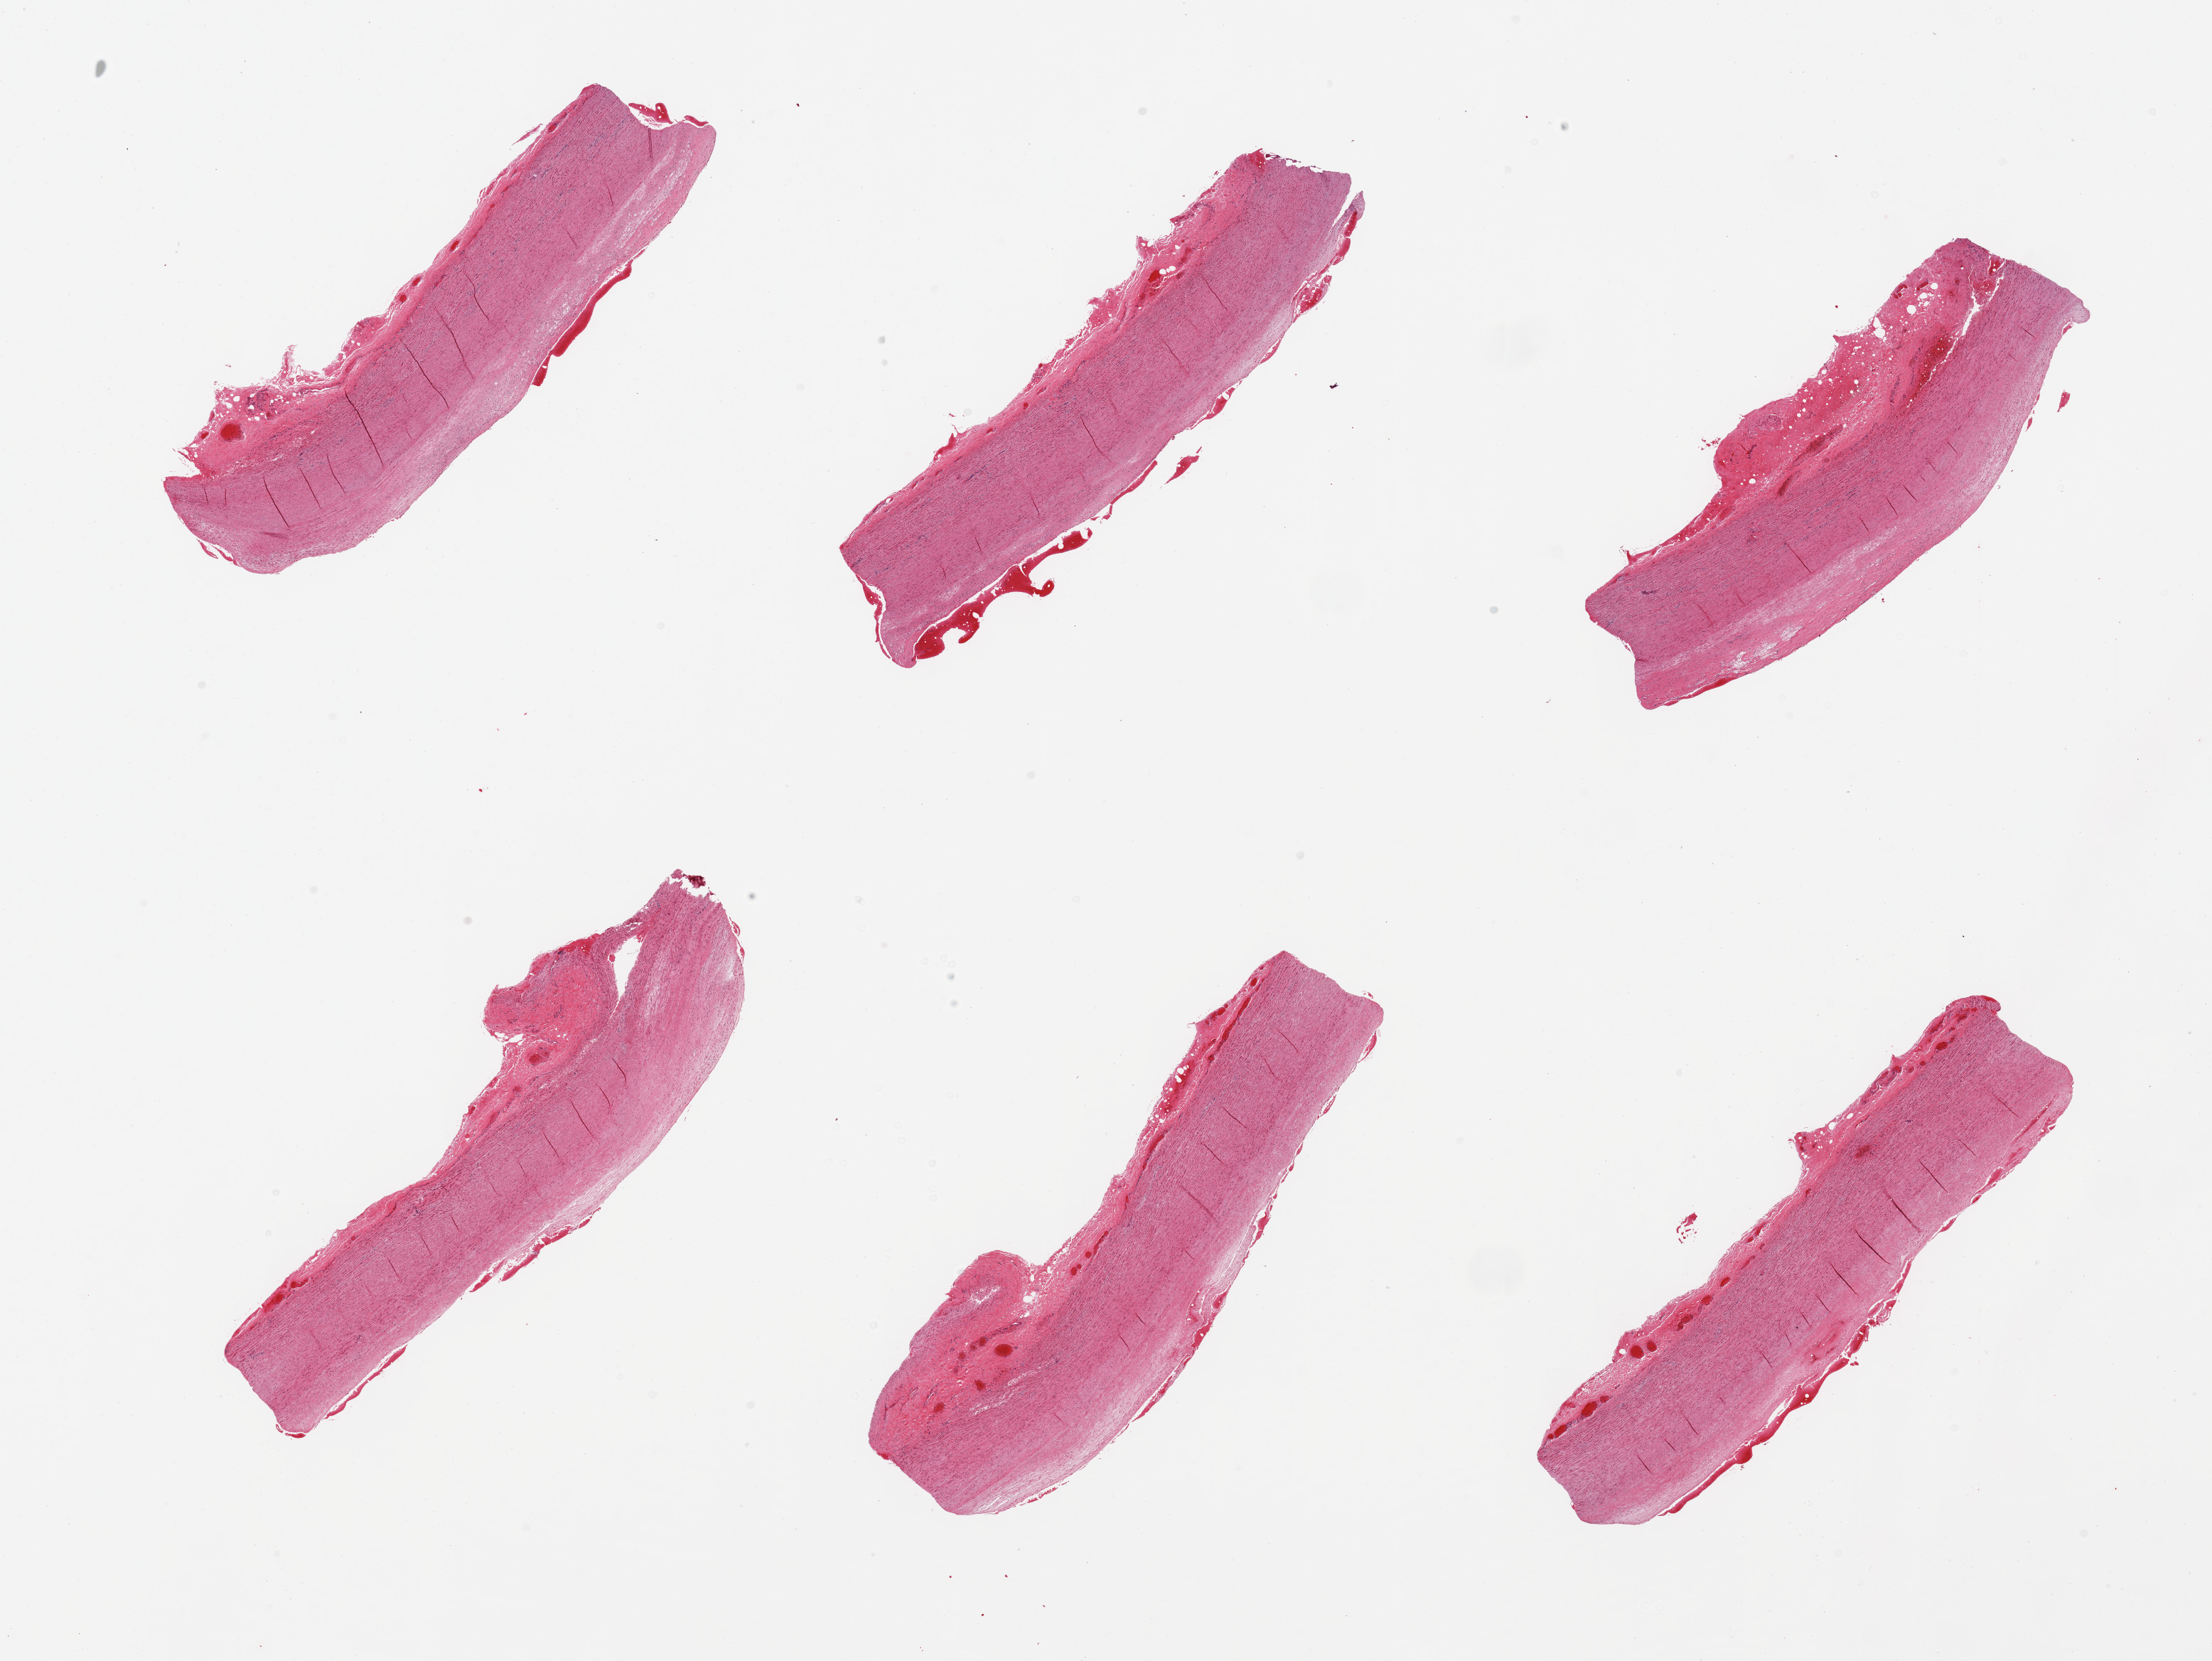
H&E whole-slide image, brightfield — shown as a low-resolution overview of the whole scanned area (about 24.6 x 18.5 mm). PAXgene-fixed paraffin-embedded (PFPE) section. Section of aorta (target tissue). Tissue donor sample. Donor sex: male.
Review note (as recorded): 6 pieces, atherosis up to ~0.5mm.